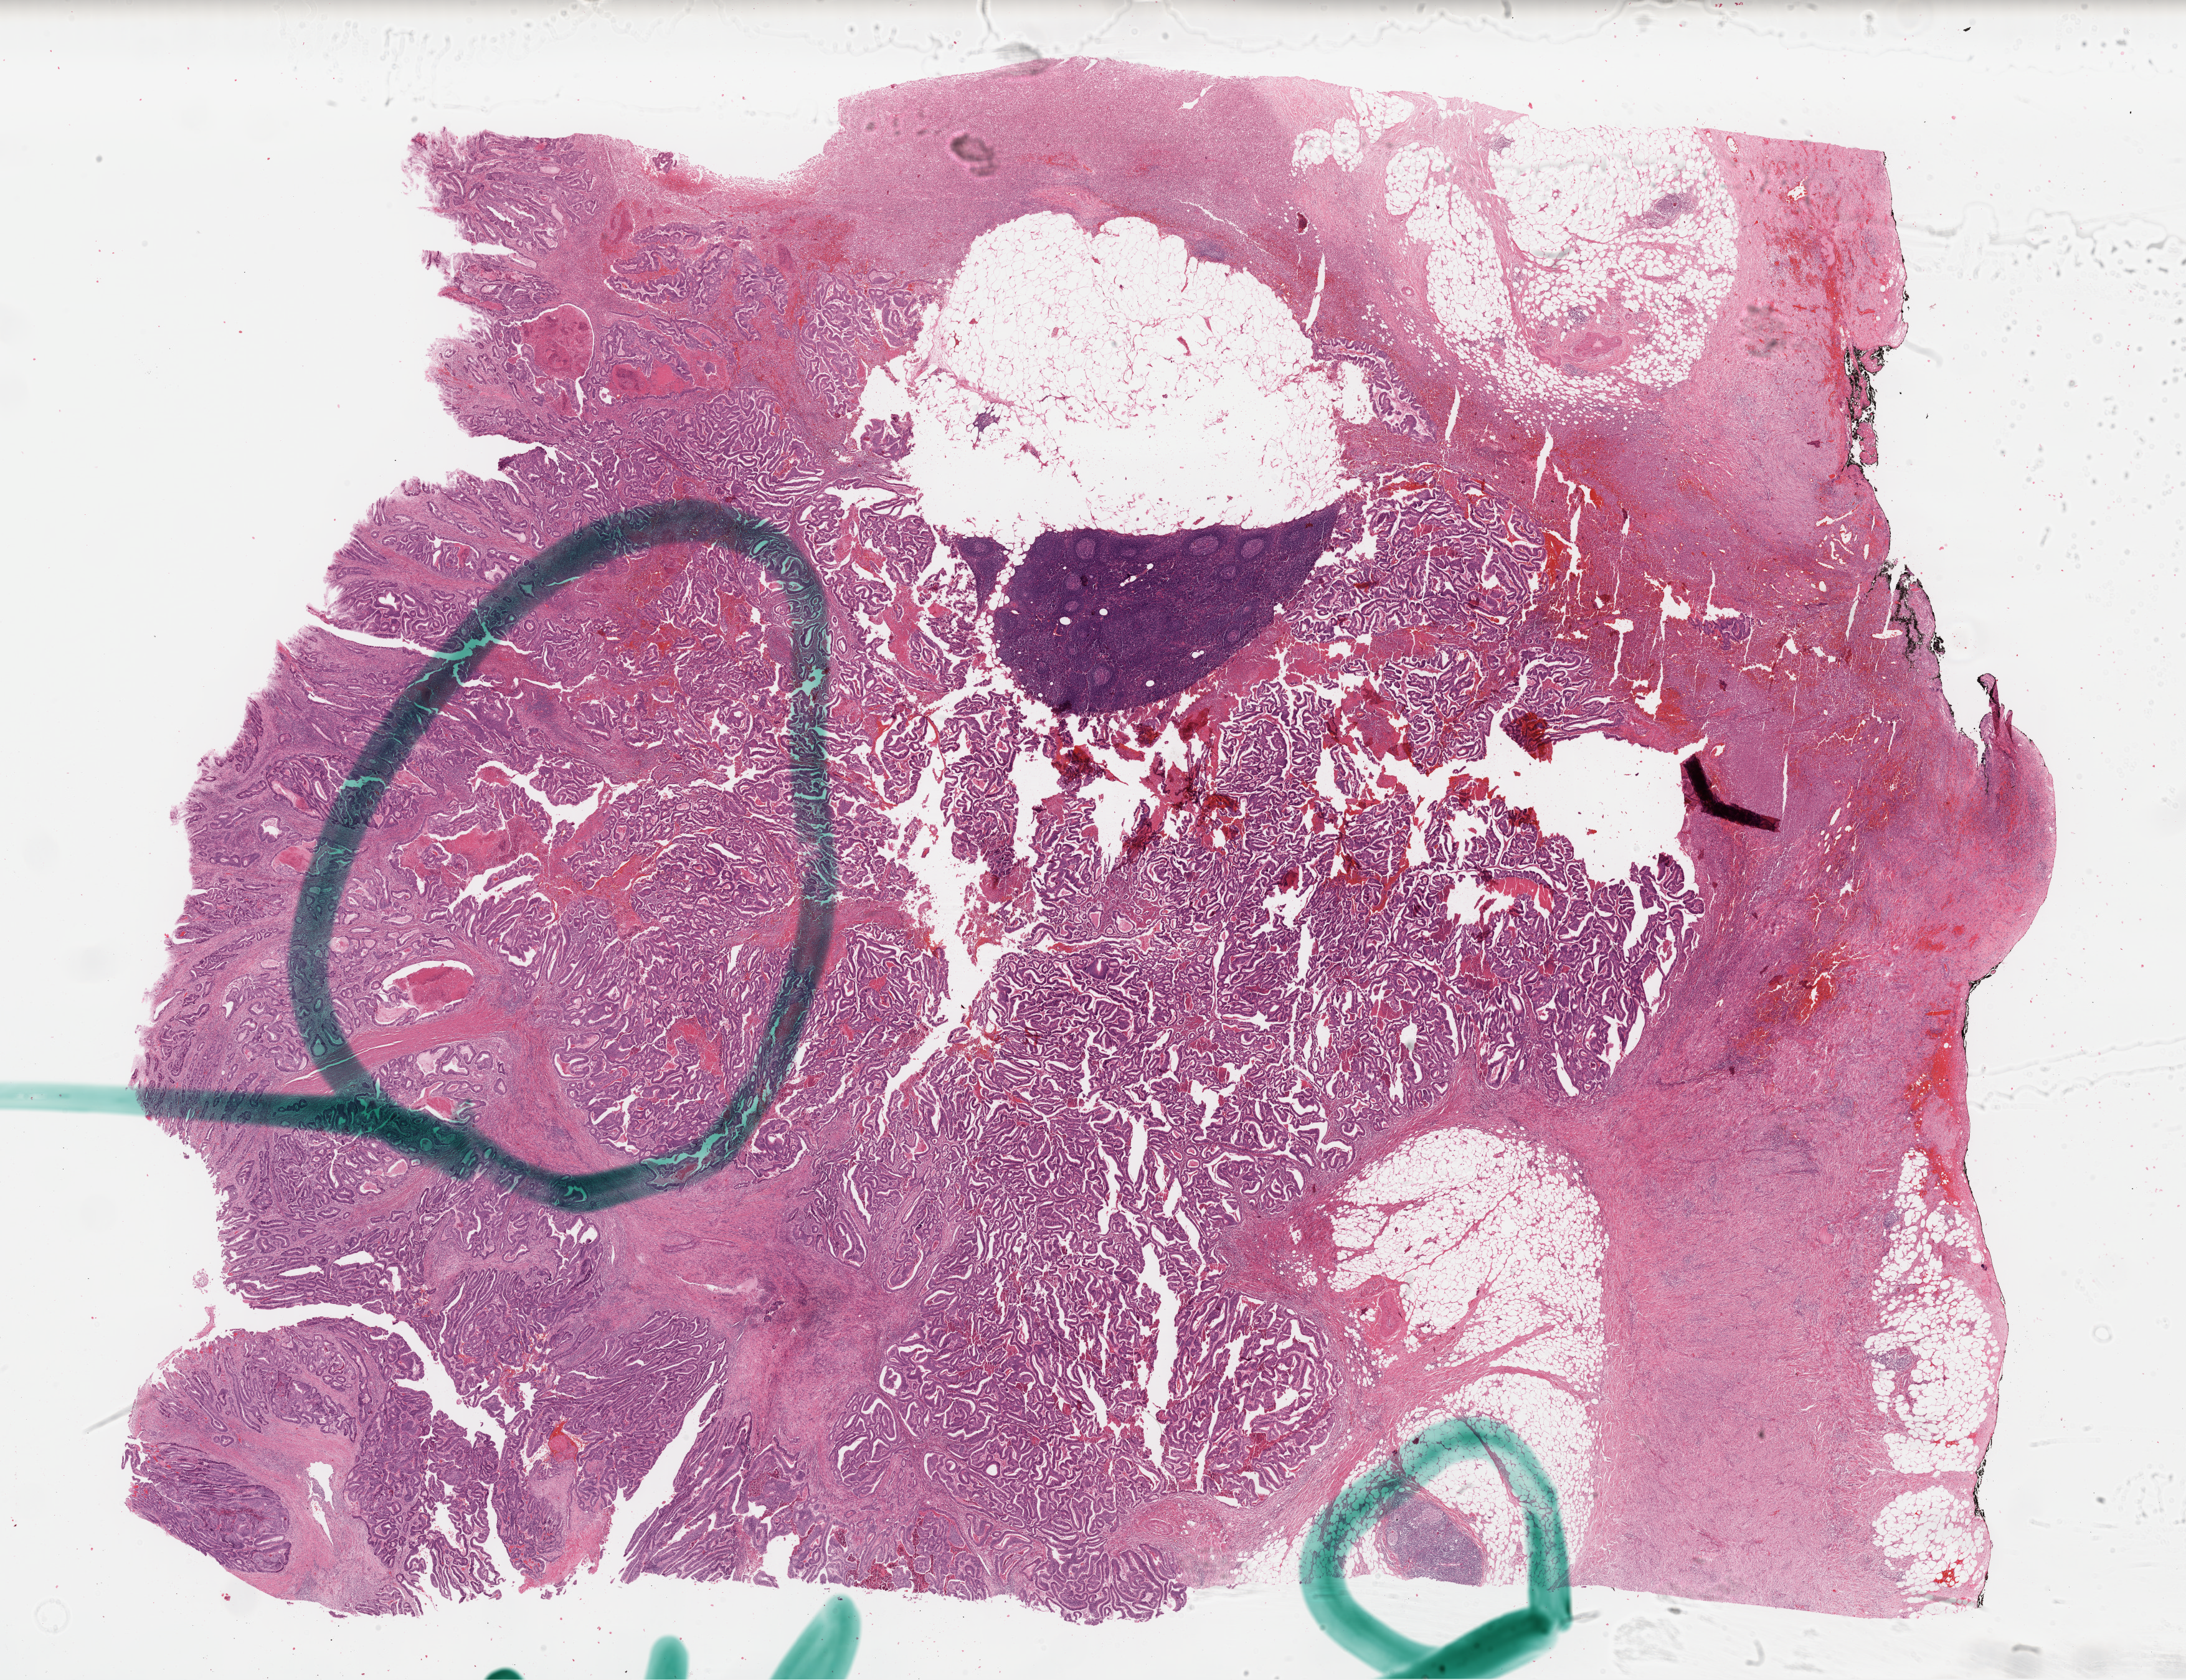
H&E-stained whole-slide image, a low-resolution overview of the entire scanned area, about 27.7 x 21.3 mm (slide scanned at 40x); formalin-fixed paraffin-embedded (FFPE) diagnostic section; primary tumour sample from the colon. Male patient; age at initial diagnosis 68 years.
AJCC pathologic stage: IIA. Lymph nodes positive (case pathology): 0 of 7 examined. Diagnosis: Adenocarcinoma, NOS (sigmoid colon). TNM: T3 N0 M0.